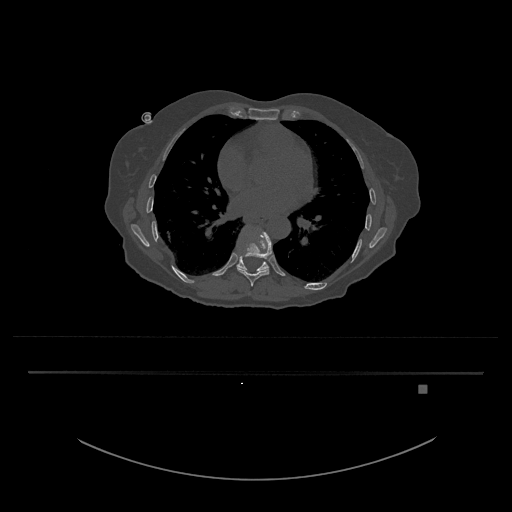
CT including the spine, one axial slice. Slice 744 of 797 in the series (ordered by position). 120 kVp. Bone window (W 1800 / L 400 HU). 0.5 mm slice thickness. 512 × 512 image matrix. Patient: female, 57 years. Case-level facts recorded for this patient, not image findings: primary cancer: cervical.
Structures marked on this image (semi-automatically segmented with operator editing):
- T10 vertebra: bounding box <237,256,269,272> (left, top, right, bottom; pixels)
- T9 vertebra: <237,233,272,287>